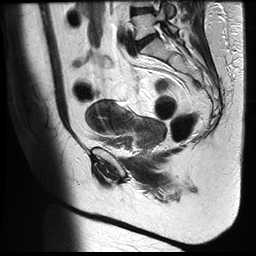
Pelvic MRI for cervical cancer, one sagittal slice. Position 13 of 35 along the scan axis. T2-weighted. 1.5 T. TE 122.8 ms, TR 4992 ms. 4 mm slice thickness. 256 × 256 image matrix, field of view 300 × 300 mm. Patient: female, 42 years.
Annotated regions visible in this slice (outlined manually by an expert reader):
- uterus and cervix: bounding box <86,99,166,148> (left, top, right, bottom; pixels)